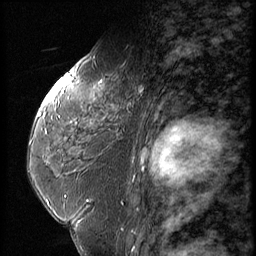
Breast MRI (dynamic contrast-enhanced), one sagittal slice; position 34 of 56 along the scan axis; dynamic contrast-enhanced series, image 2 of 3 at this slice position (ordered by acquisition); 1.5 T; TE 4.2 ms, TR 9 ms; 256 × 256 image matrix, field of view 180 × 180 mm. Patient: female, 59 years. Case-level facts recorded for this patient, not image findings: setting: breast cancer imaged before/during neoadjuvant chemotherapy; receptor status: HER2-positive.
Outlined on this slice (semi-automatic segmentation, software-assisted and operator-edited):
- analysis volume of interest (the breast-tissue region the enhancement analysis was run in; not a lesion): bounding box (x1, y1, x2, y2) in pixels: (44, 66, 151, 135)
- tumour enhancement mask (voxels above the 140 % enhancement threshold inside the analysis volume of interest): (44, 66, 103, 105)